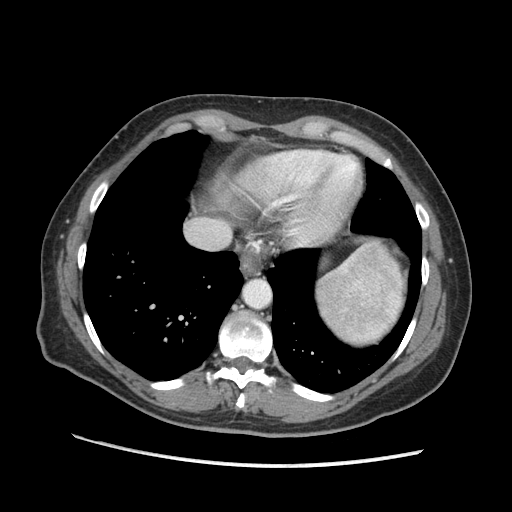
Contrast-enhanced abdominal CT (liver protocol), one axial slice. Position 157 of 170 along the scan axis. Reconstruction kernel STANDARD. 140 kVp. Soft-tissue window (W 400 / L 40 HU). 2.5 mm slice thickness. 512 × 512 image matrix, field of view 360 × 360 mm. From the clinical record (not read from this slice): diagnosis: hepatocellular carcinoma (patient treated with transarterial chemoembolisation; whether this scan precedes or follows treatment is not stated here); TNM stage (as recorded): Stage-II; Child-Pugh class: A; tumour differentiation: no biopsy; tumour size: 4 cm.
Outlined on this slice (semi-automatic segmentation, software-assisted and operator-edited):
- abdominal aorta: box from (x=246, y=281) to (x=269, y=307) px